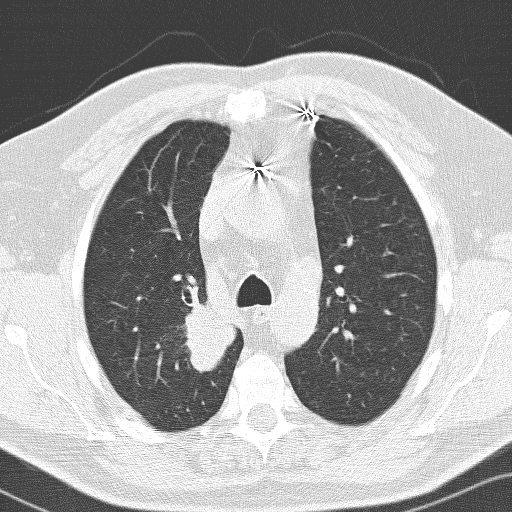
Low-dose screening chest CT, axial slice; baseline annual screen; lung window (W 1500 / L -600 HU); 3.2 mm slice thickness. Male, age 66 years at enrolment. Former smoker at enrolment.
Expert-annotated lung lesion, box from (x=148, y=299) to (x=232, y=390) px. The exam's reader record, not a measurement of the box and not confirmed to be the same lesion: non-calcified nodule or mass ≥4 mm, right upper lobe, 36 × 30 mm, spiculated (stellate) margins, soft tissue attenuation. Official screen result: positive, change unspecified: nodule(s) >= 4 mm or enlarging nodule(s), mass(es), or other non-specific abnormalities suspicious for lung cancer. Lung cancer was diagnosed 103 days after this screen: adenocarcinoma, NOS, right upper lobe, poorly differentiated (G3), stage IIB (AJCC 6th edition), 33 mm at pathology.